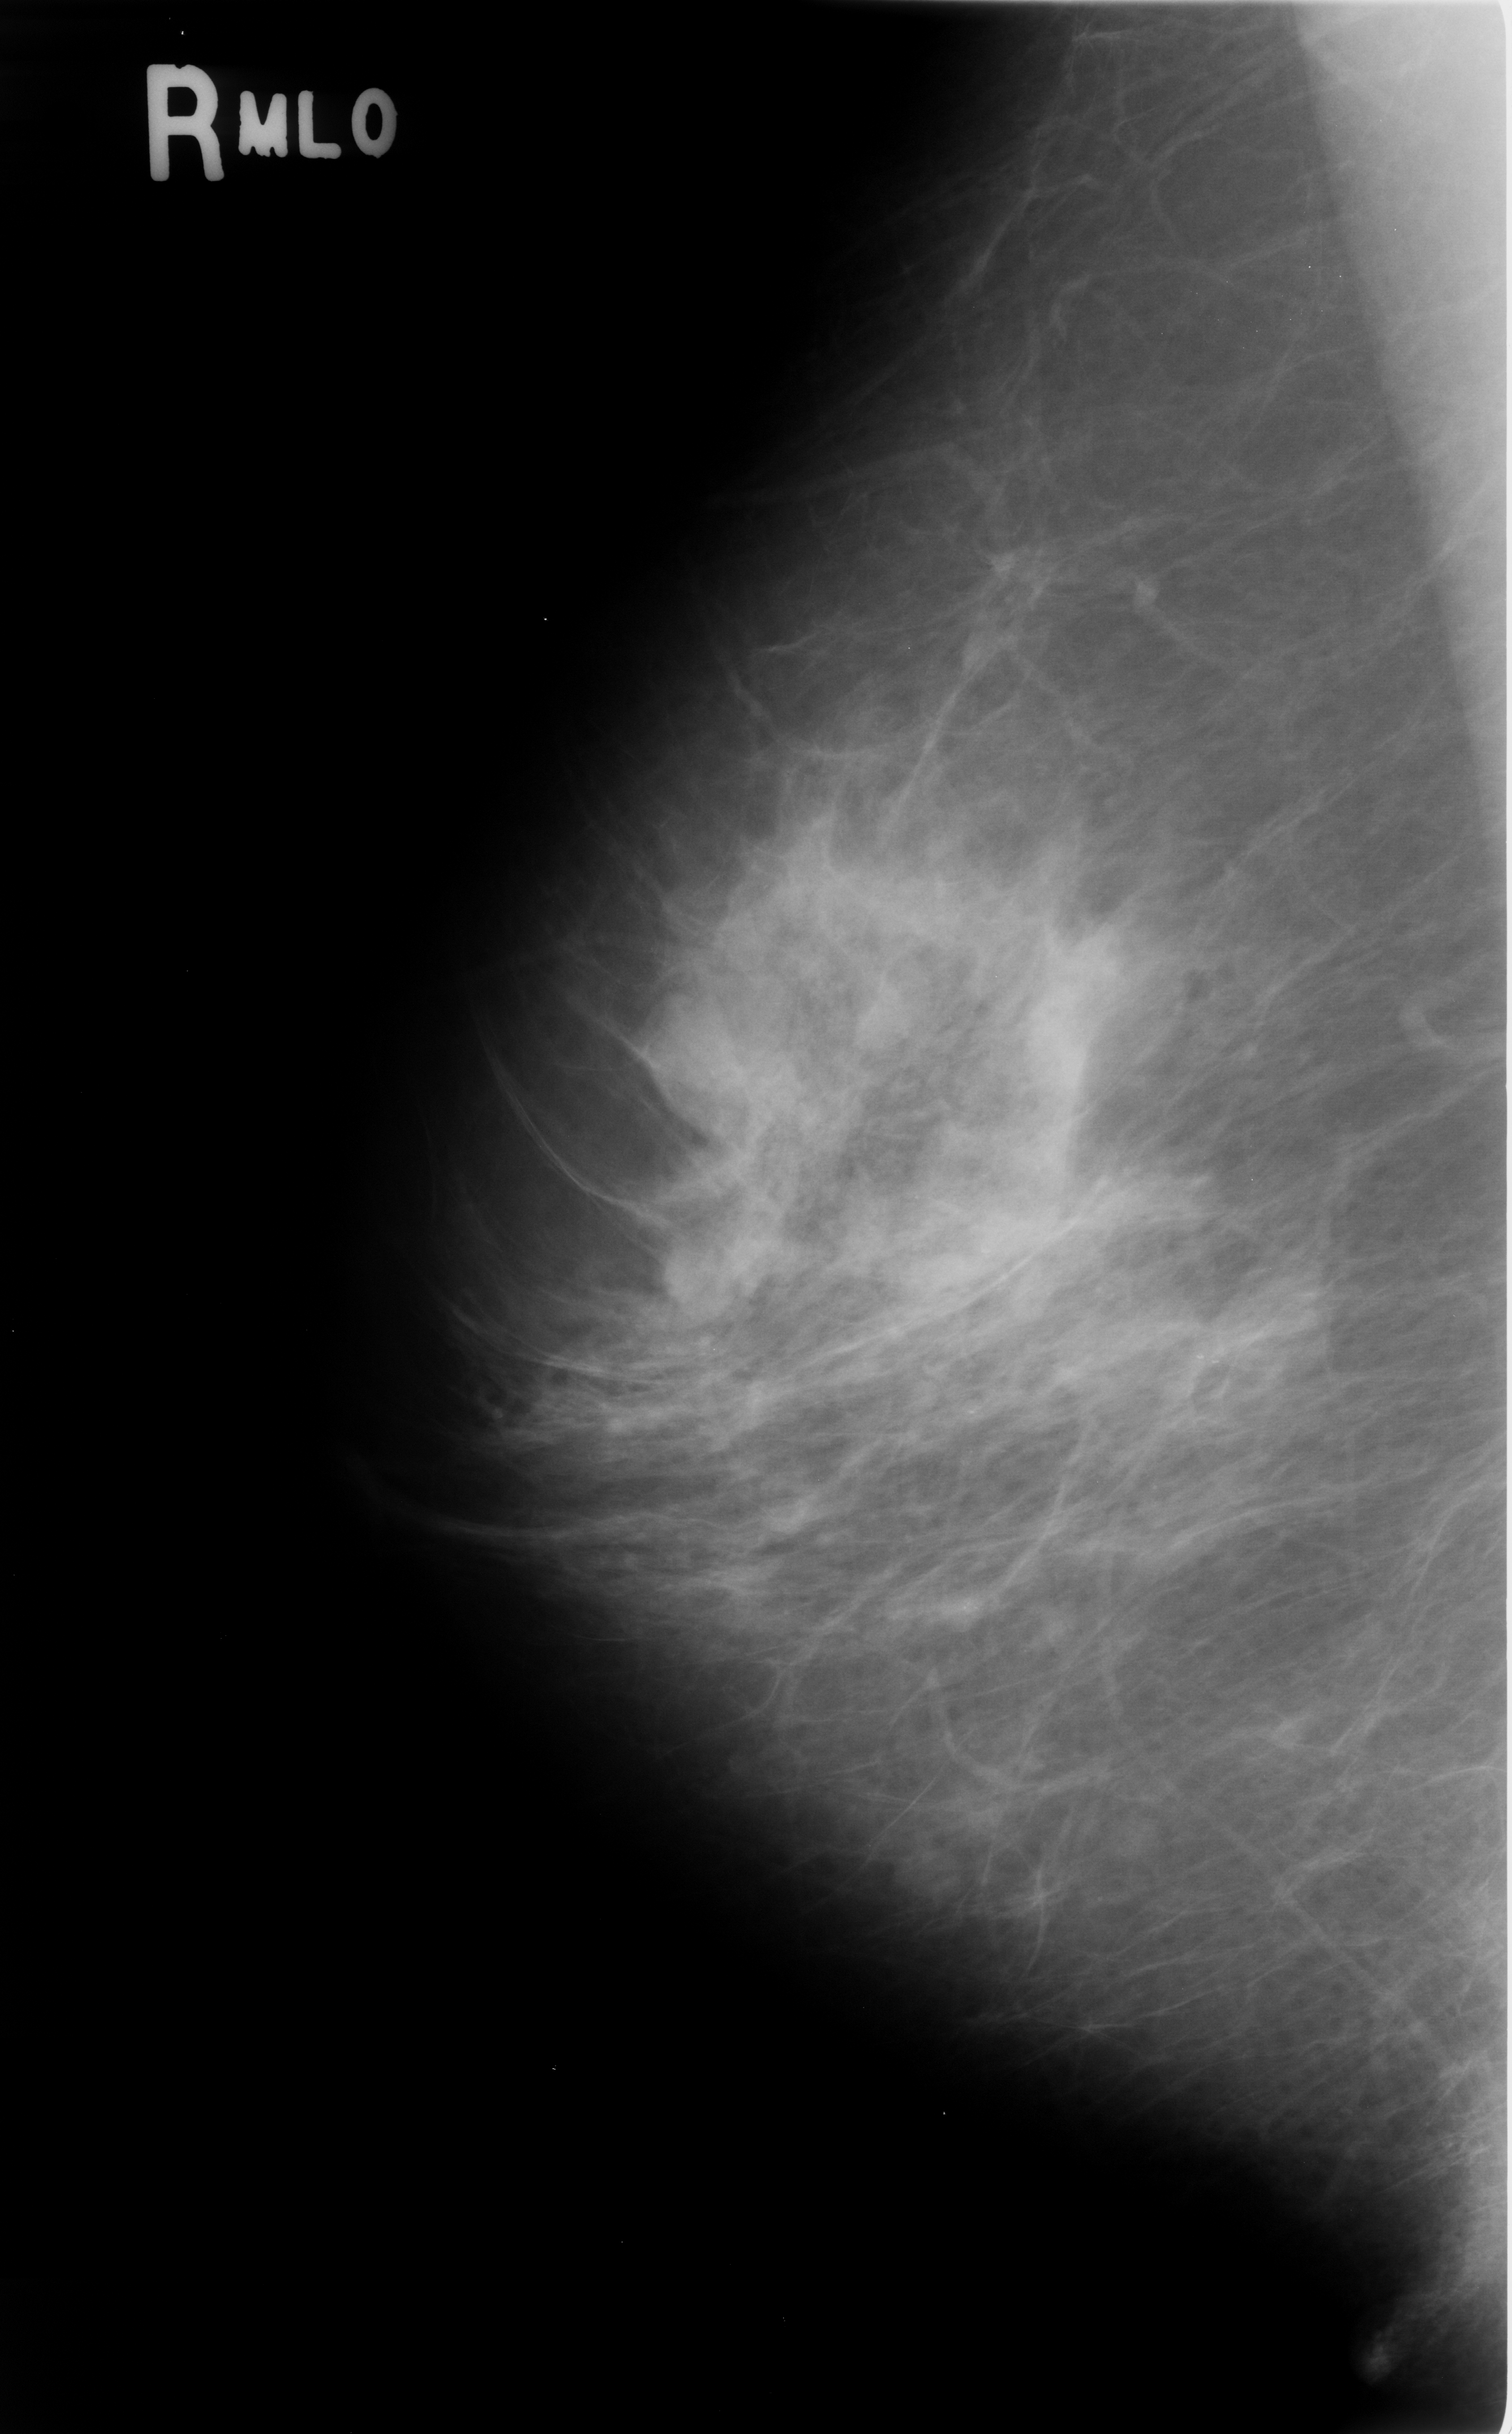
Digitized screen-film mammogram; right breast; MLO view; breast composition: scattered fibroglandular densities (BI-RADS density category 2 of 4).
- Marked findings (only marked abnormalities are described; nothing is implied about the rest of the image): mass, shape oval, margins circumscribed; BI-RADS assessment category 4; pathology result (as recorded, not read from the image): benign.